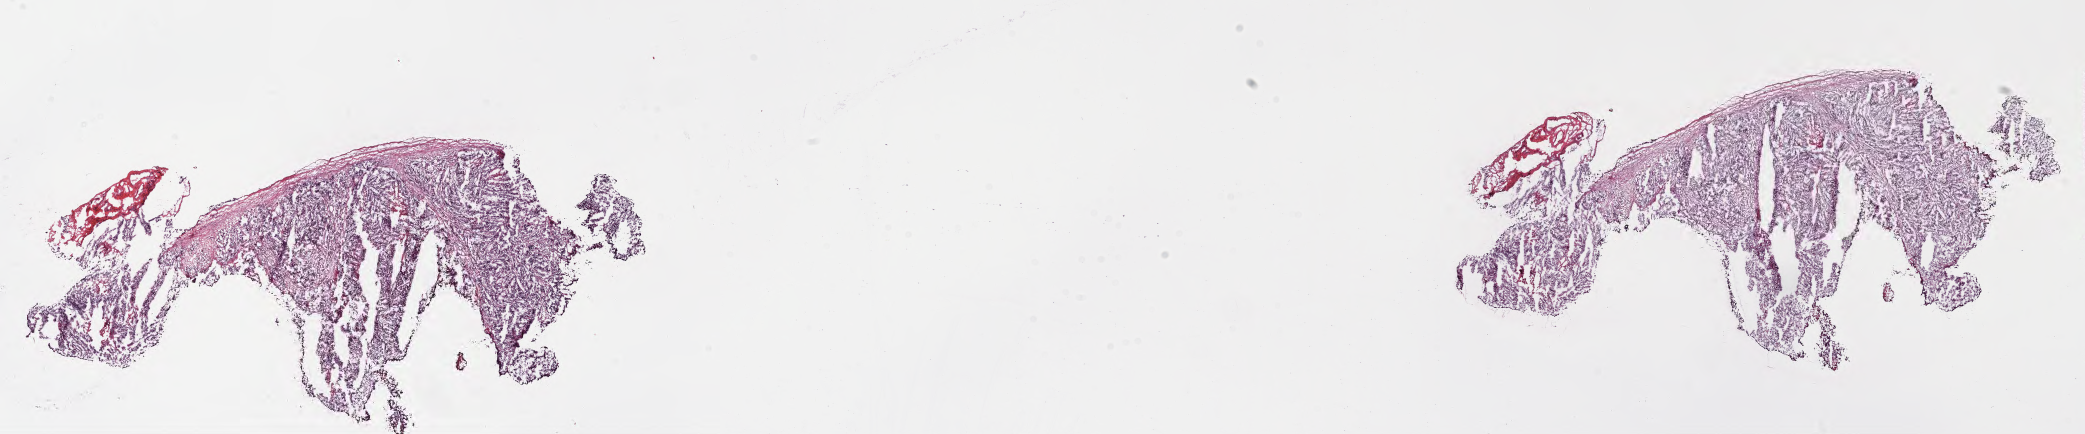
Digitized haematoxylin and eosin-stained section of tumor tissue from the adrenal gland — low-resolution overview of the scanned area, about 33.7 x 7.0 mm; frozen section. Female patient, age 39 months.
* diagnosis (ICD-O-3 morphology term): Neuroblastoma, NOS